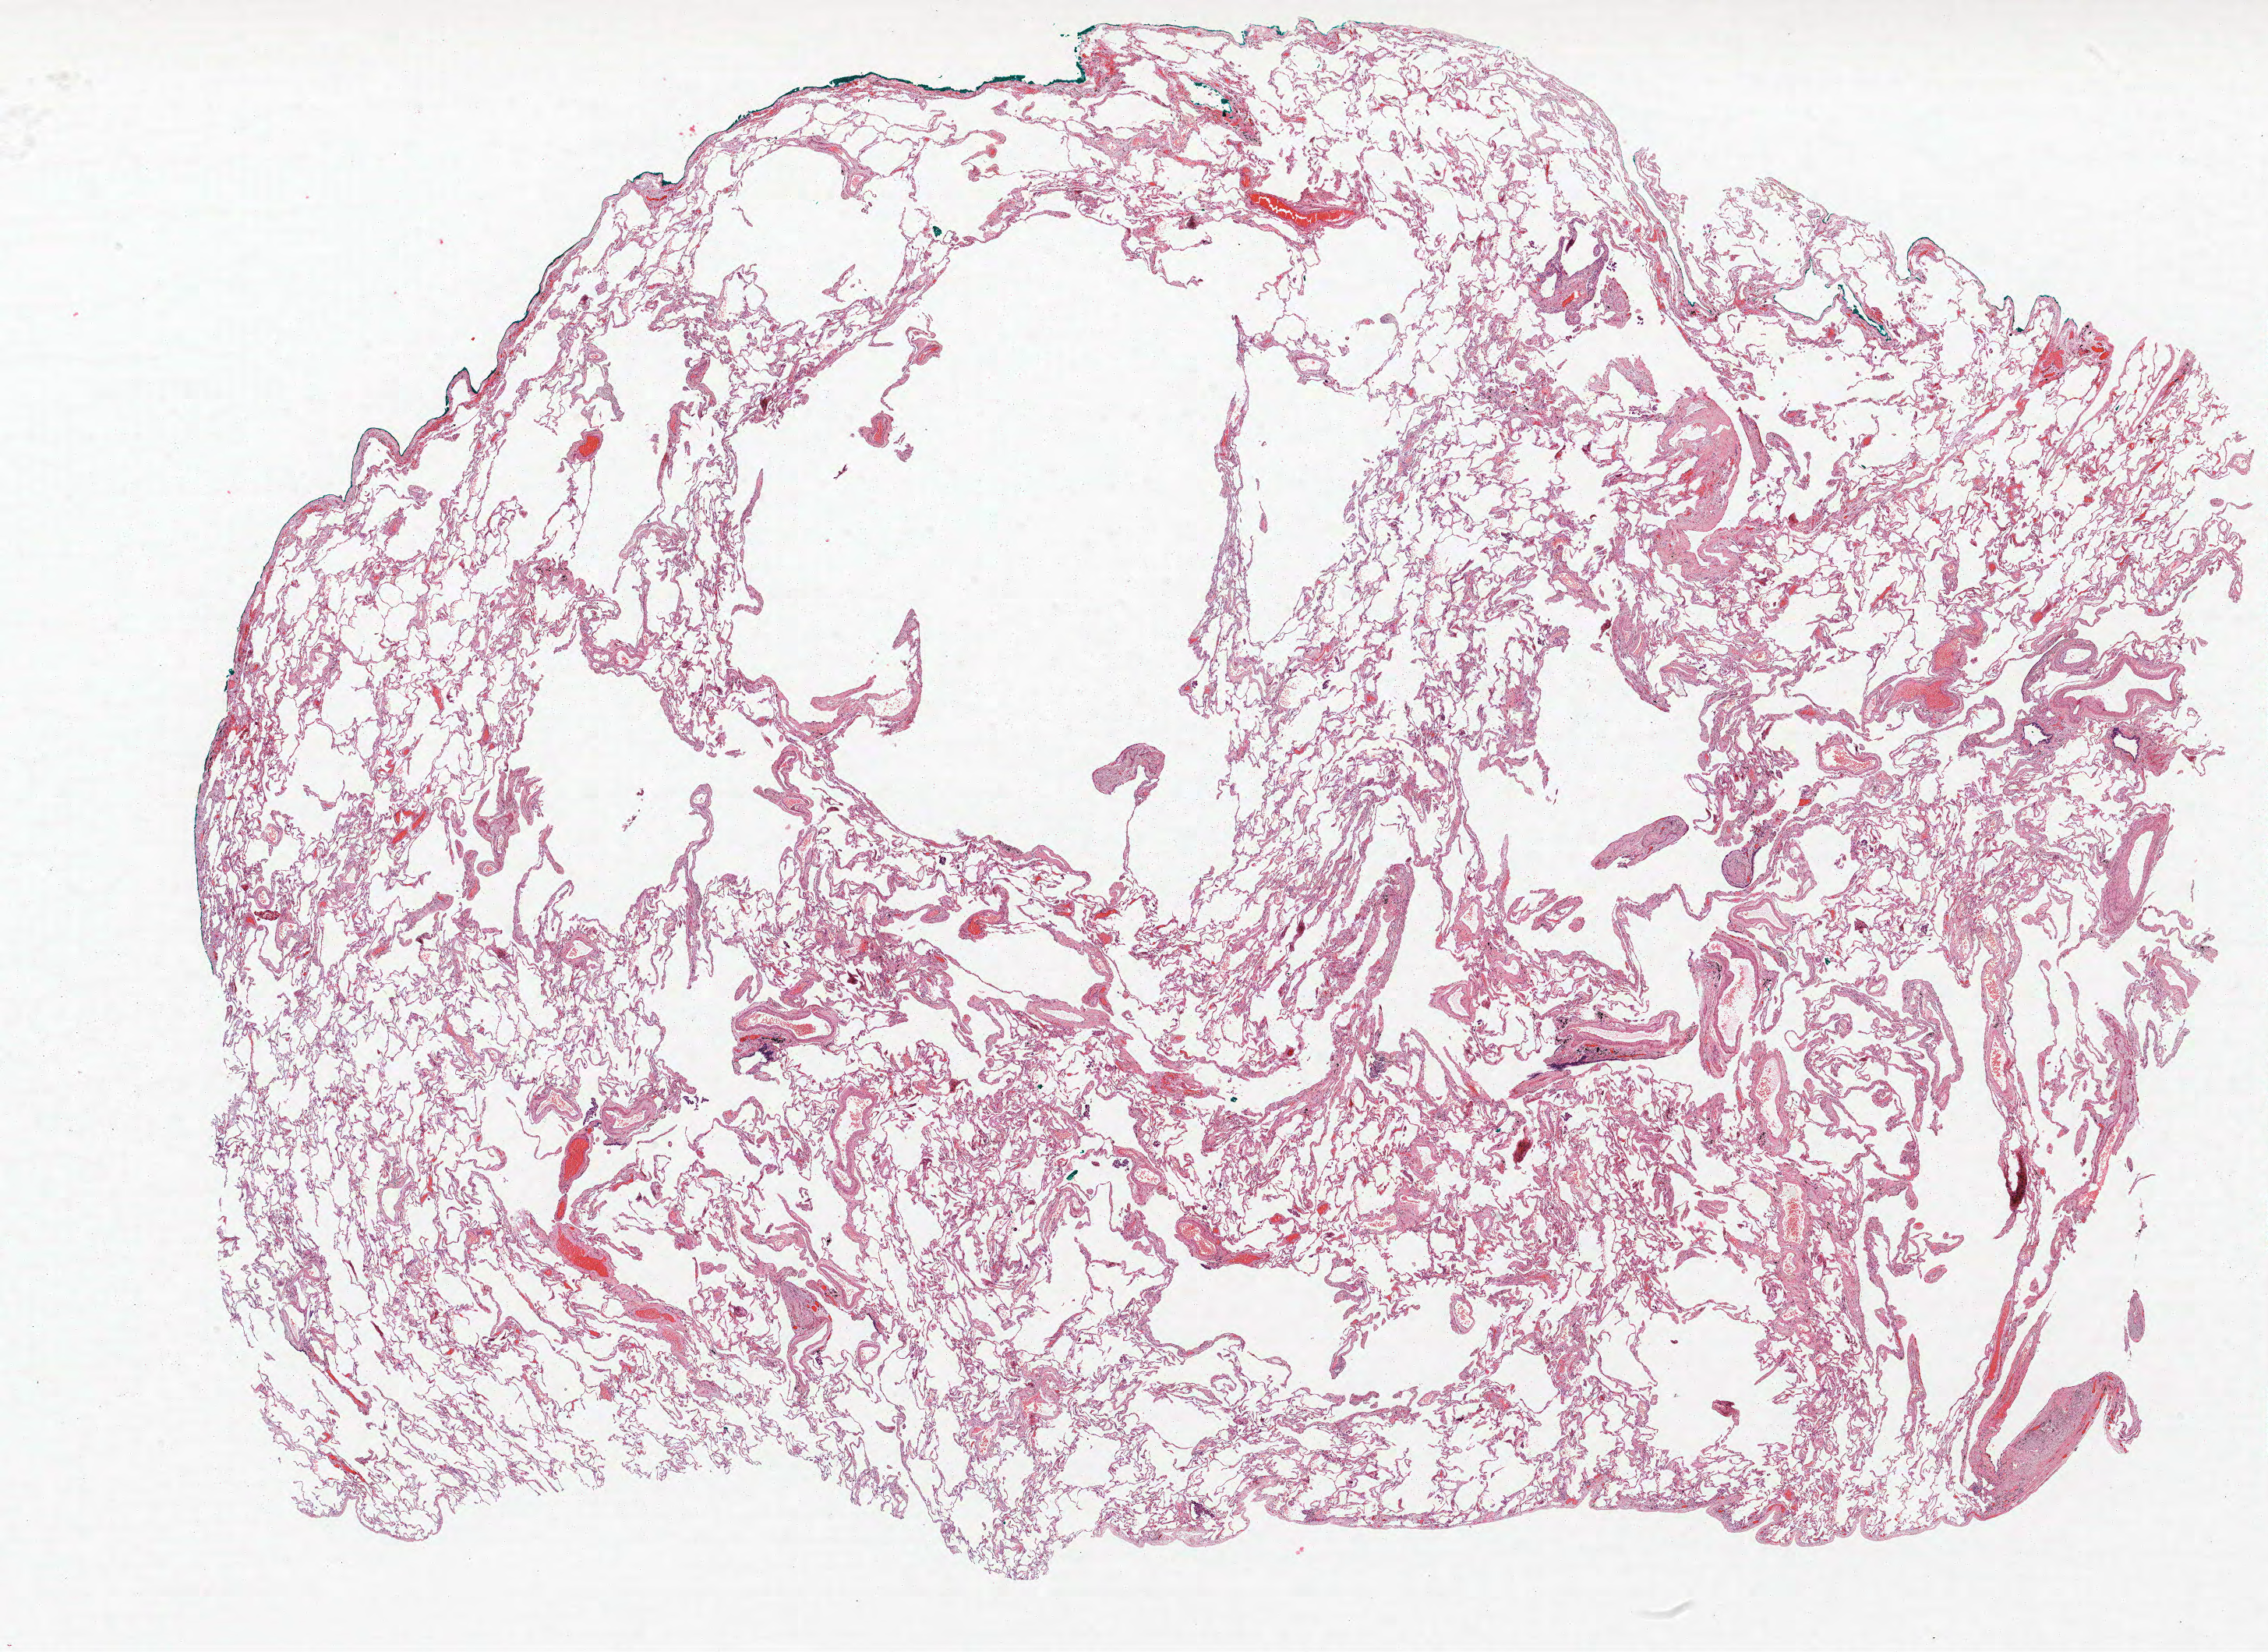
H&E whole-slide image — low-resolution overview of the scanned area, about 23.3 x 17.0 mm (from a 40x scan); FFPE section; lung. Female patient, aged 73 at enrolment. Former smoker at enrolment. Grade: moderately differentiated (G2).
Tumour size (pathology): 15 mm. Stage (AJCC 6th edition): IB. Primary tumour location (clinical record): right upper lobe. Participant's lung-cancer diagnosis: Adenocarcinoma, NOS.